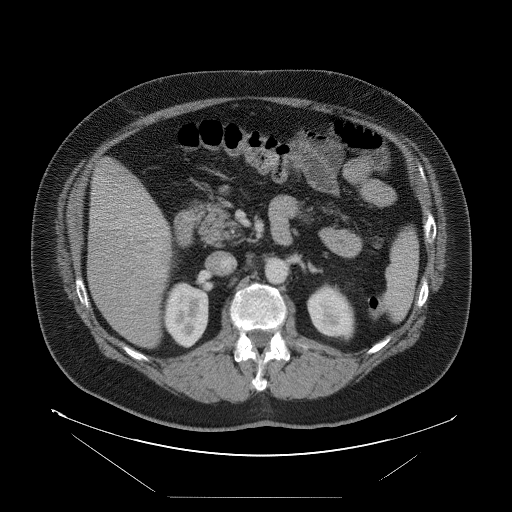
Contrast-enhanced abdominal CT, one axial slice; position 41 of 114 along the scan axis; 120 kVp; intravenous contrast given; soft-tissue window (W 400 / L 40 HU); 512 × 512 image matrix. Male patient, age 61 years. Case-level facts recorded for this patient, not image findings: diagnosis: colorectal cancer liver metastases, imaged before liver resection; multiple liver metastases: no; largest metastasis: 6.5 cm; disease in both lobes: yes.
Structures marked on this image (outlined manually by an expert reader):
- liver: bounding box [x1, y1, x2, y2] px = [89, 161, 173, 348]